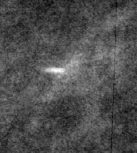
Crop from a digitized film mammogram around one marked abnormality, right breast, CC view, BI-RADS breast density category 1 (scale 1–4).
Finding: calcifications, distribution regional; BI-RADS assessment category 2; subtlety rating 3 on a 1 (subtle) to 5 (obvious) scale; benign; no additional work-up was recommended (benign without callback).